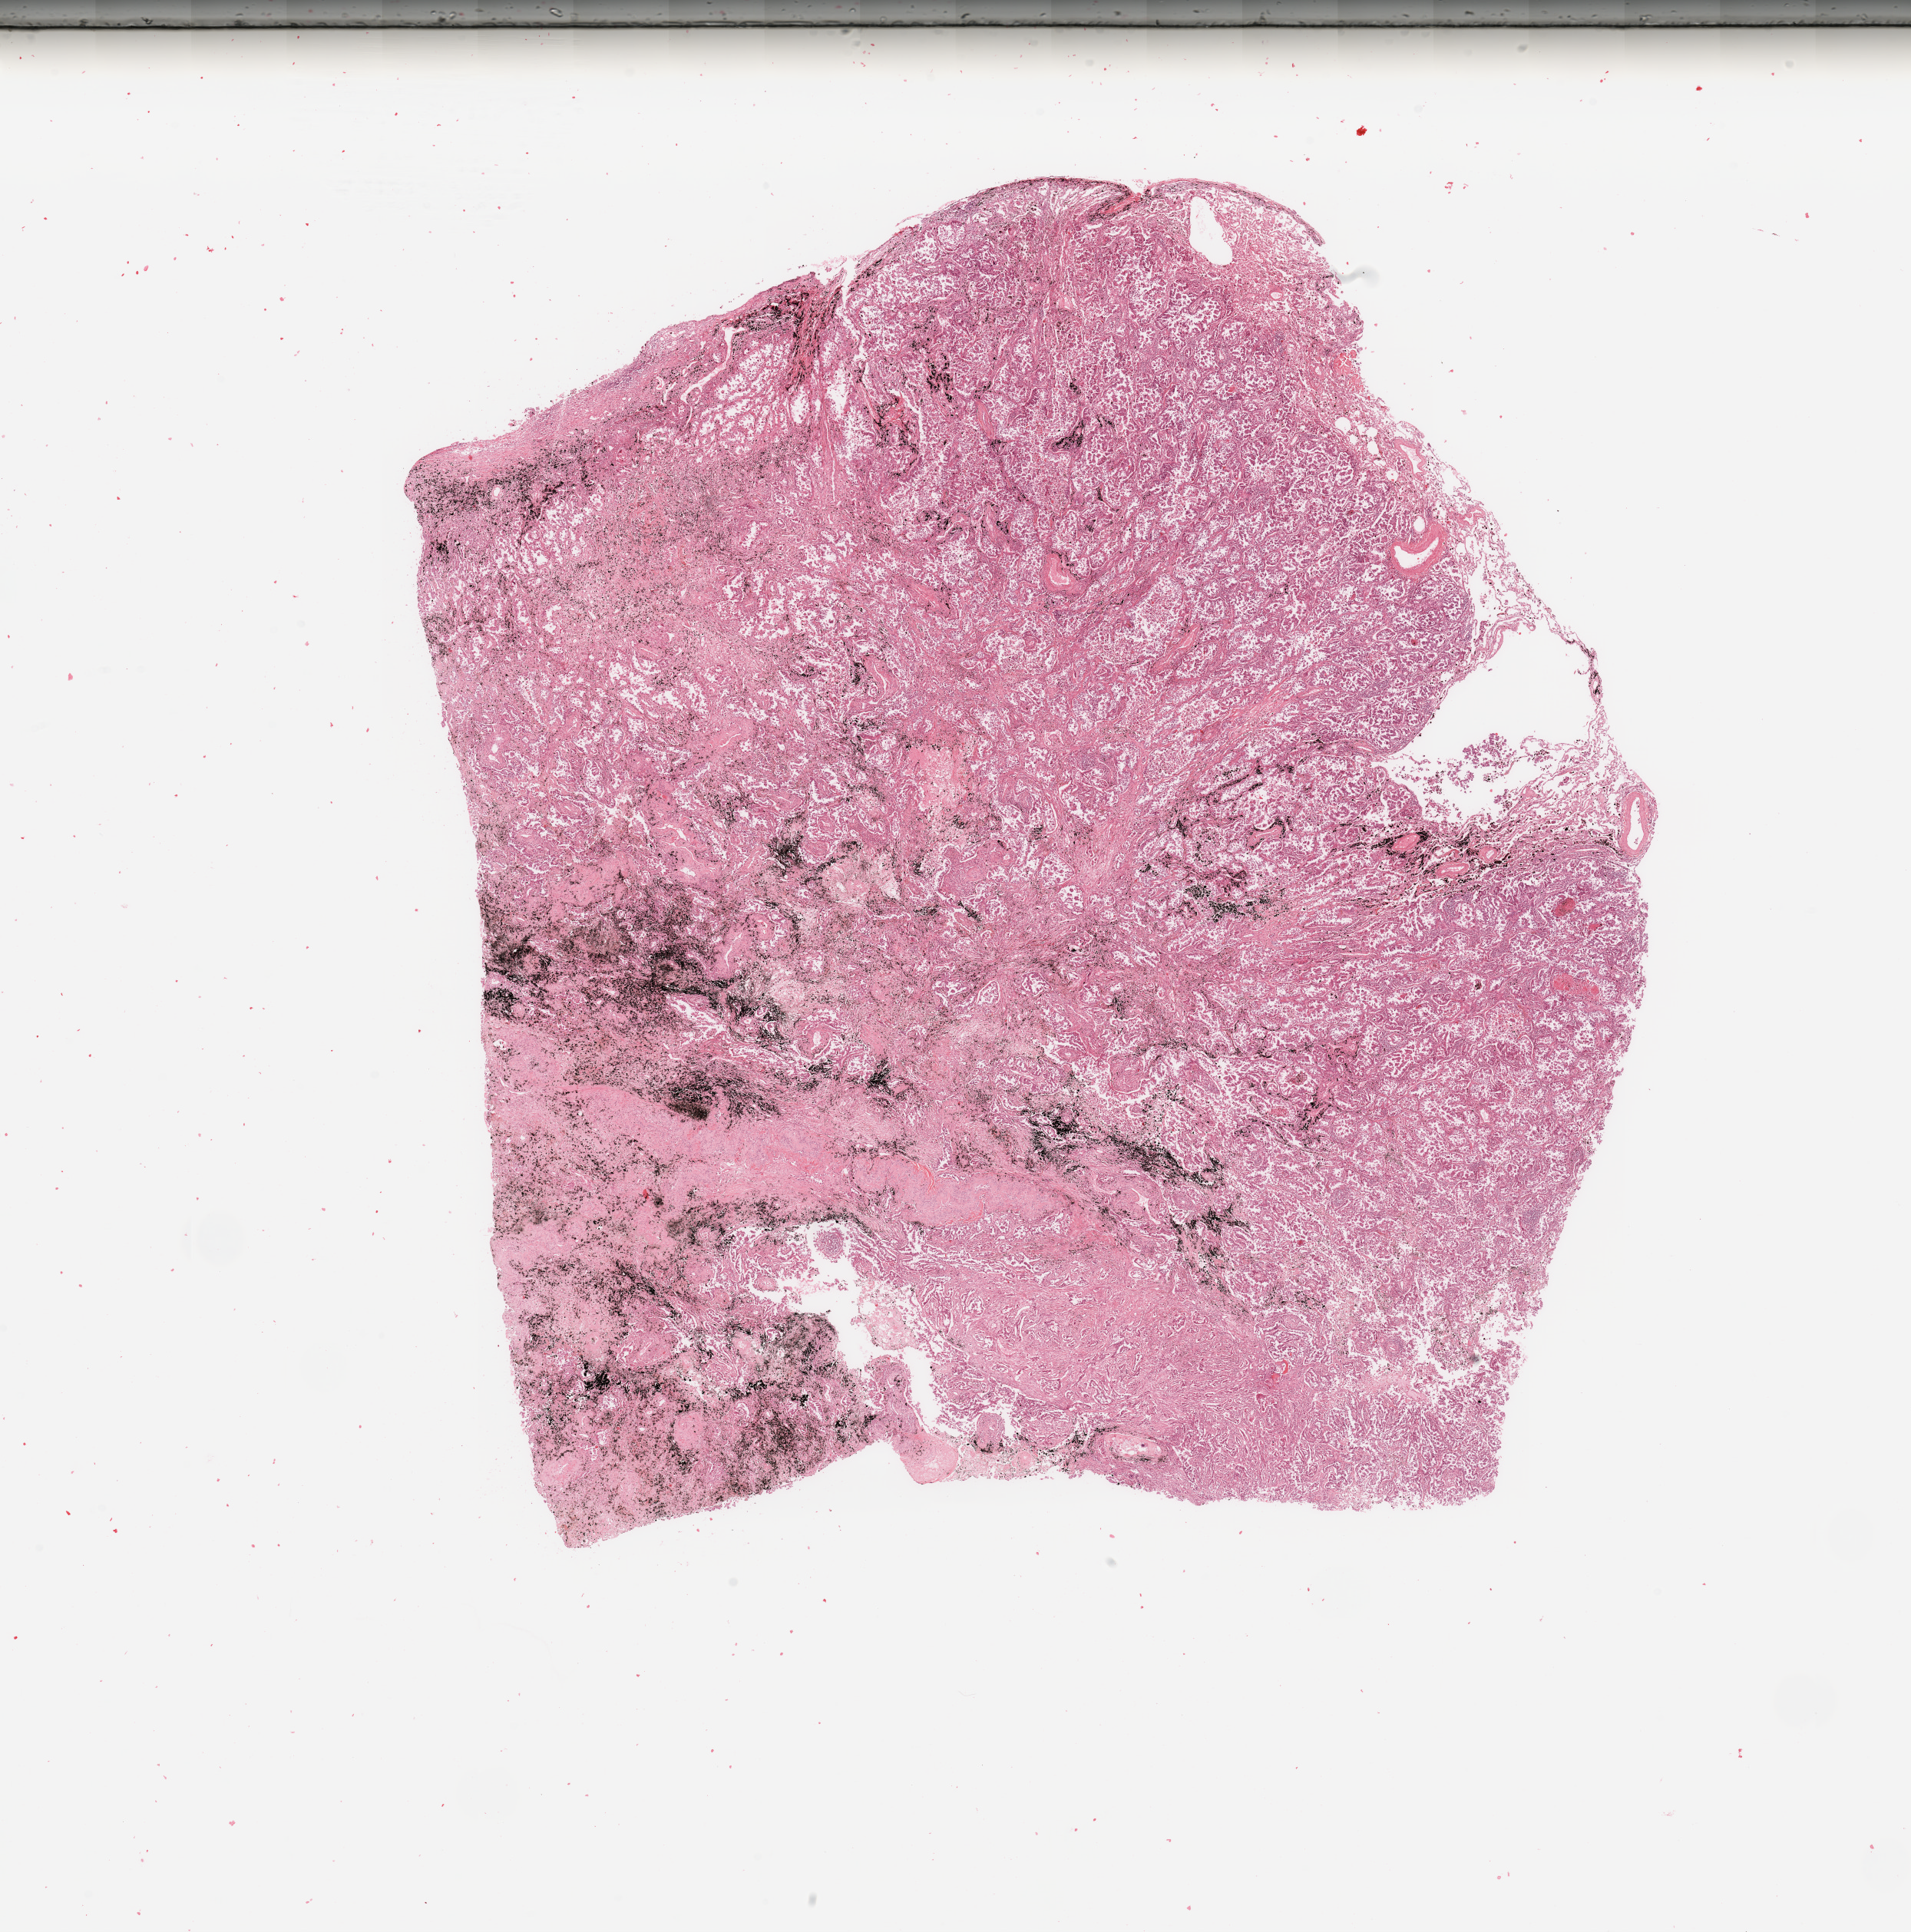
Digitized Hematoxylin and eosin (H&E) stained tissue section (whole slide), whole scanned area (about 19.7 x 19.9 mm, from a 20x scan) shown as a low-resolution overview. Lung, tumour tissue. Male, 72 y/o. Histologic grade: G2 (moderately differentiated).
AJCC pathologic stage: IB. Histologic diagnosis: Adenocarcinoma, NOS.